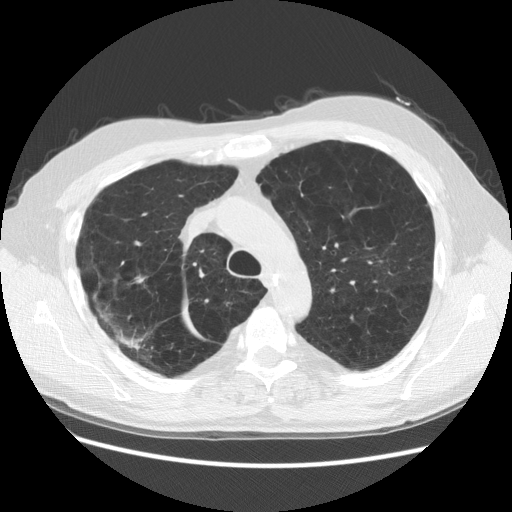
Axial slice from a low-dose chest CT screening exam. Third screening round (two years after baseline). Lung window (W 1500 / L -600 HU). 2.5 mm slice thickness. Slice 101 of 137 in the series. Male participant, aged 58 years at enrolment.
Expert reader's lesion annotation, box from (x=110, y=256) to (x=163, y=304) px. The screening reader recorded 3 non-calcified nodules or masses ≥4 mm on this exam (right lower lobe, right upper lobe, right upper lobe); which of them this box marks is not recorded. Later outcome: lung cancer diagnosed 88 days after this screen — squamous cell carcinoma, NOS, right upper lobe, moderately differentiated (G2), stage IB (AJCC 6th edition), 18 mm at pathology.